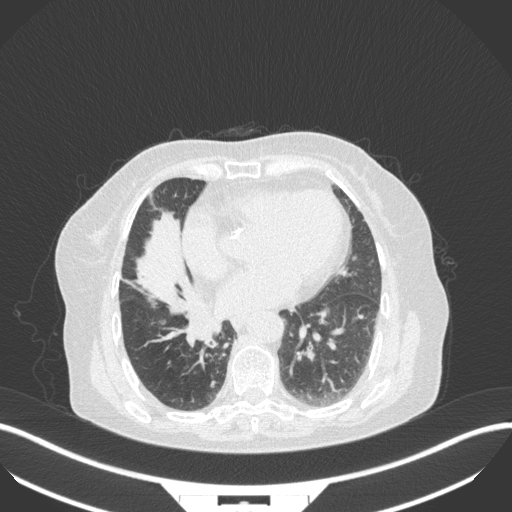
Chest CT, one axial slice; position 123 of 329 along the scan axis; reconstruction kernel B31f; lung window (W 1500 / L -600 HU); 1 mm slice thickness; 512 × 512 image matrix, field of view 400 × 400 mm. Female patient, age 75 years. Case-level facts recorded for this patient, not image findings: clinical TNM (as recorded): T1b N0 M1a; histopathological grade: G1.
Outlined on this slice (rectangle marked by the reading radiologist):
- lung tumour (recorded histology: squamous cell carcinoma): bounding box [x1, y1, x2, y2] px = [185, 308, 224, 349]